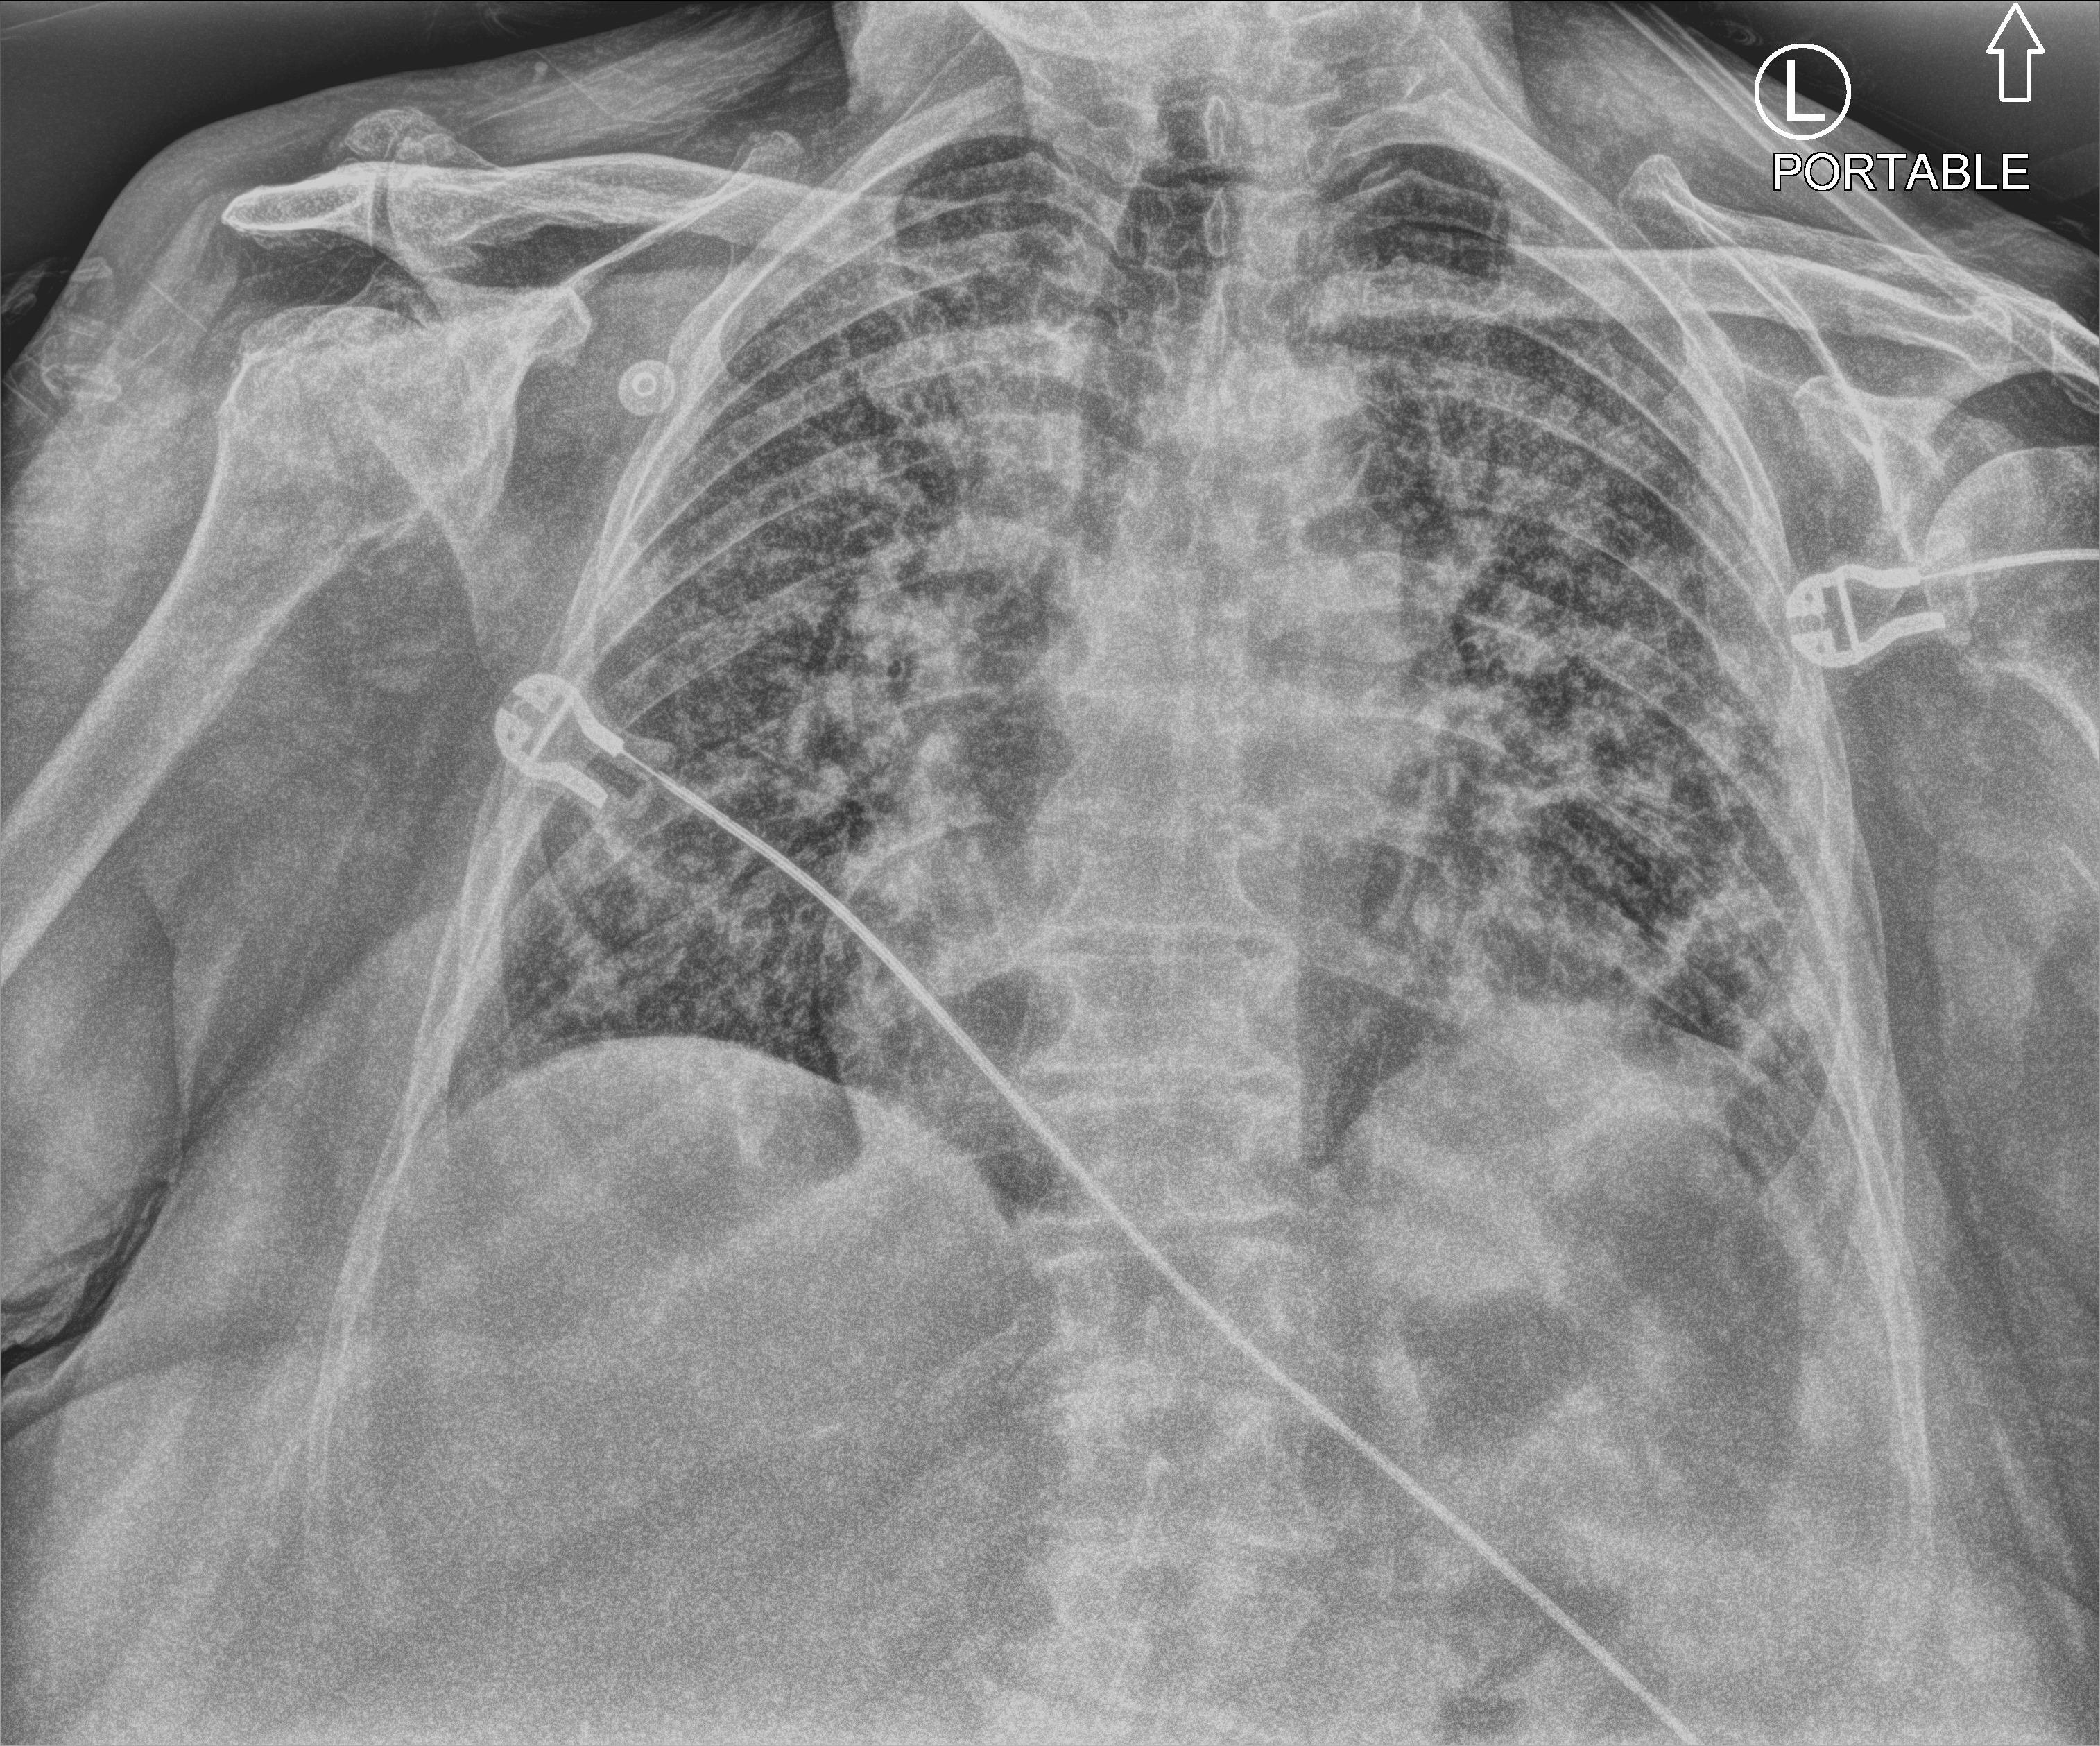
Bedside chest radiograph (computed radiography), anteroposterior (AP) projection. Patient hospitalised with COVID-19; female, aged 60–74 years.
From the hospital-stay record, not from the radiograph (when in the stay this image was taken is not recorded): mechanically ventilated during this hospital stay: no.